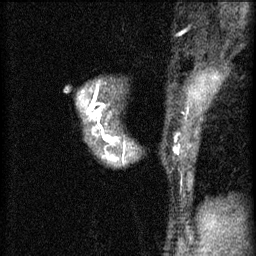
Breast MRI (dynamic contrast-enhanced), one sagittal slice. 3 images stored at this slice position (order not interpretable as contrast timing). 1.5 T. TE 4.2 ms, TR 11 ms. 256 × 256 image matrix, field of view 180 × 180 mm. Patient: female, 37 years.
Annotated regions visible in this slice (semi-automatic segmentation, software-assisted and operator-edited):
- analysis volume of interest (the breast-tissue region the enhancement analysis was run in; not a lesion): bounding box <85,118,135,165> (left, top, right, bottom; pixels)
- tumour enhancement mask (voxels above the 70 % enhancement threshold inside the analysis volume of interest): <97,118,125,161>